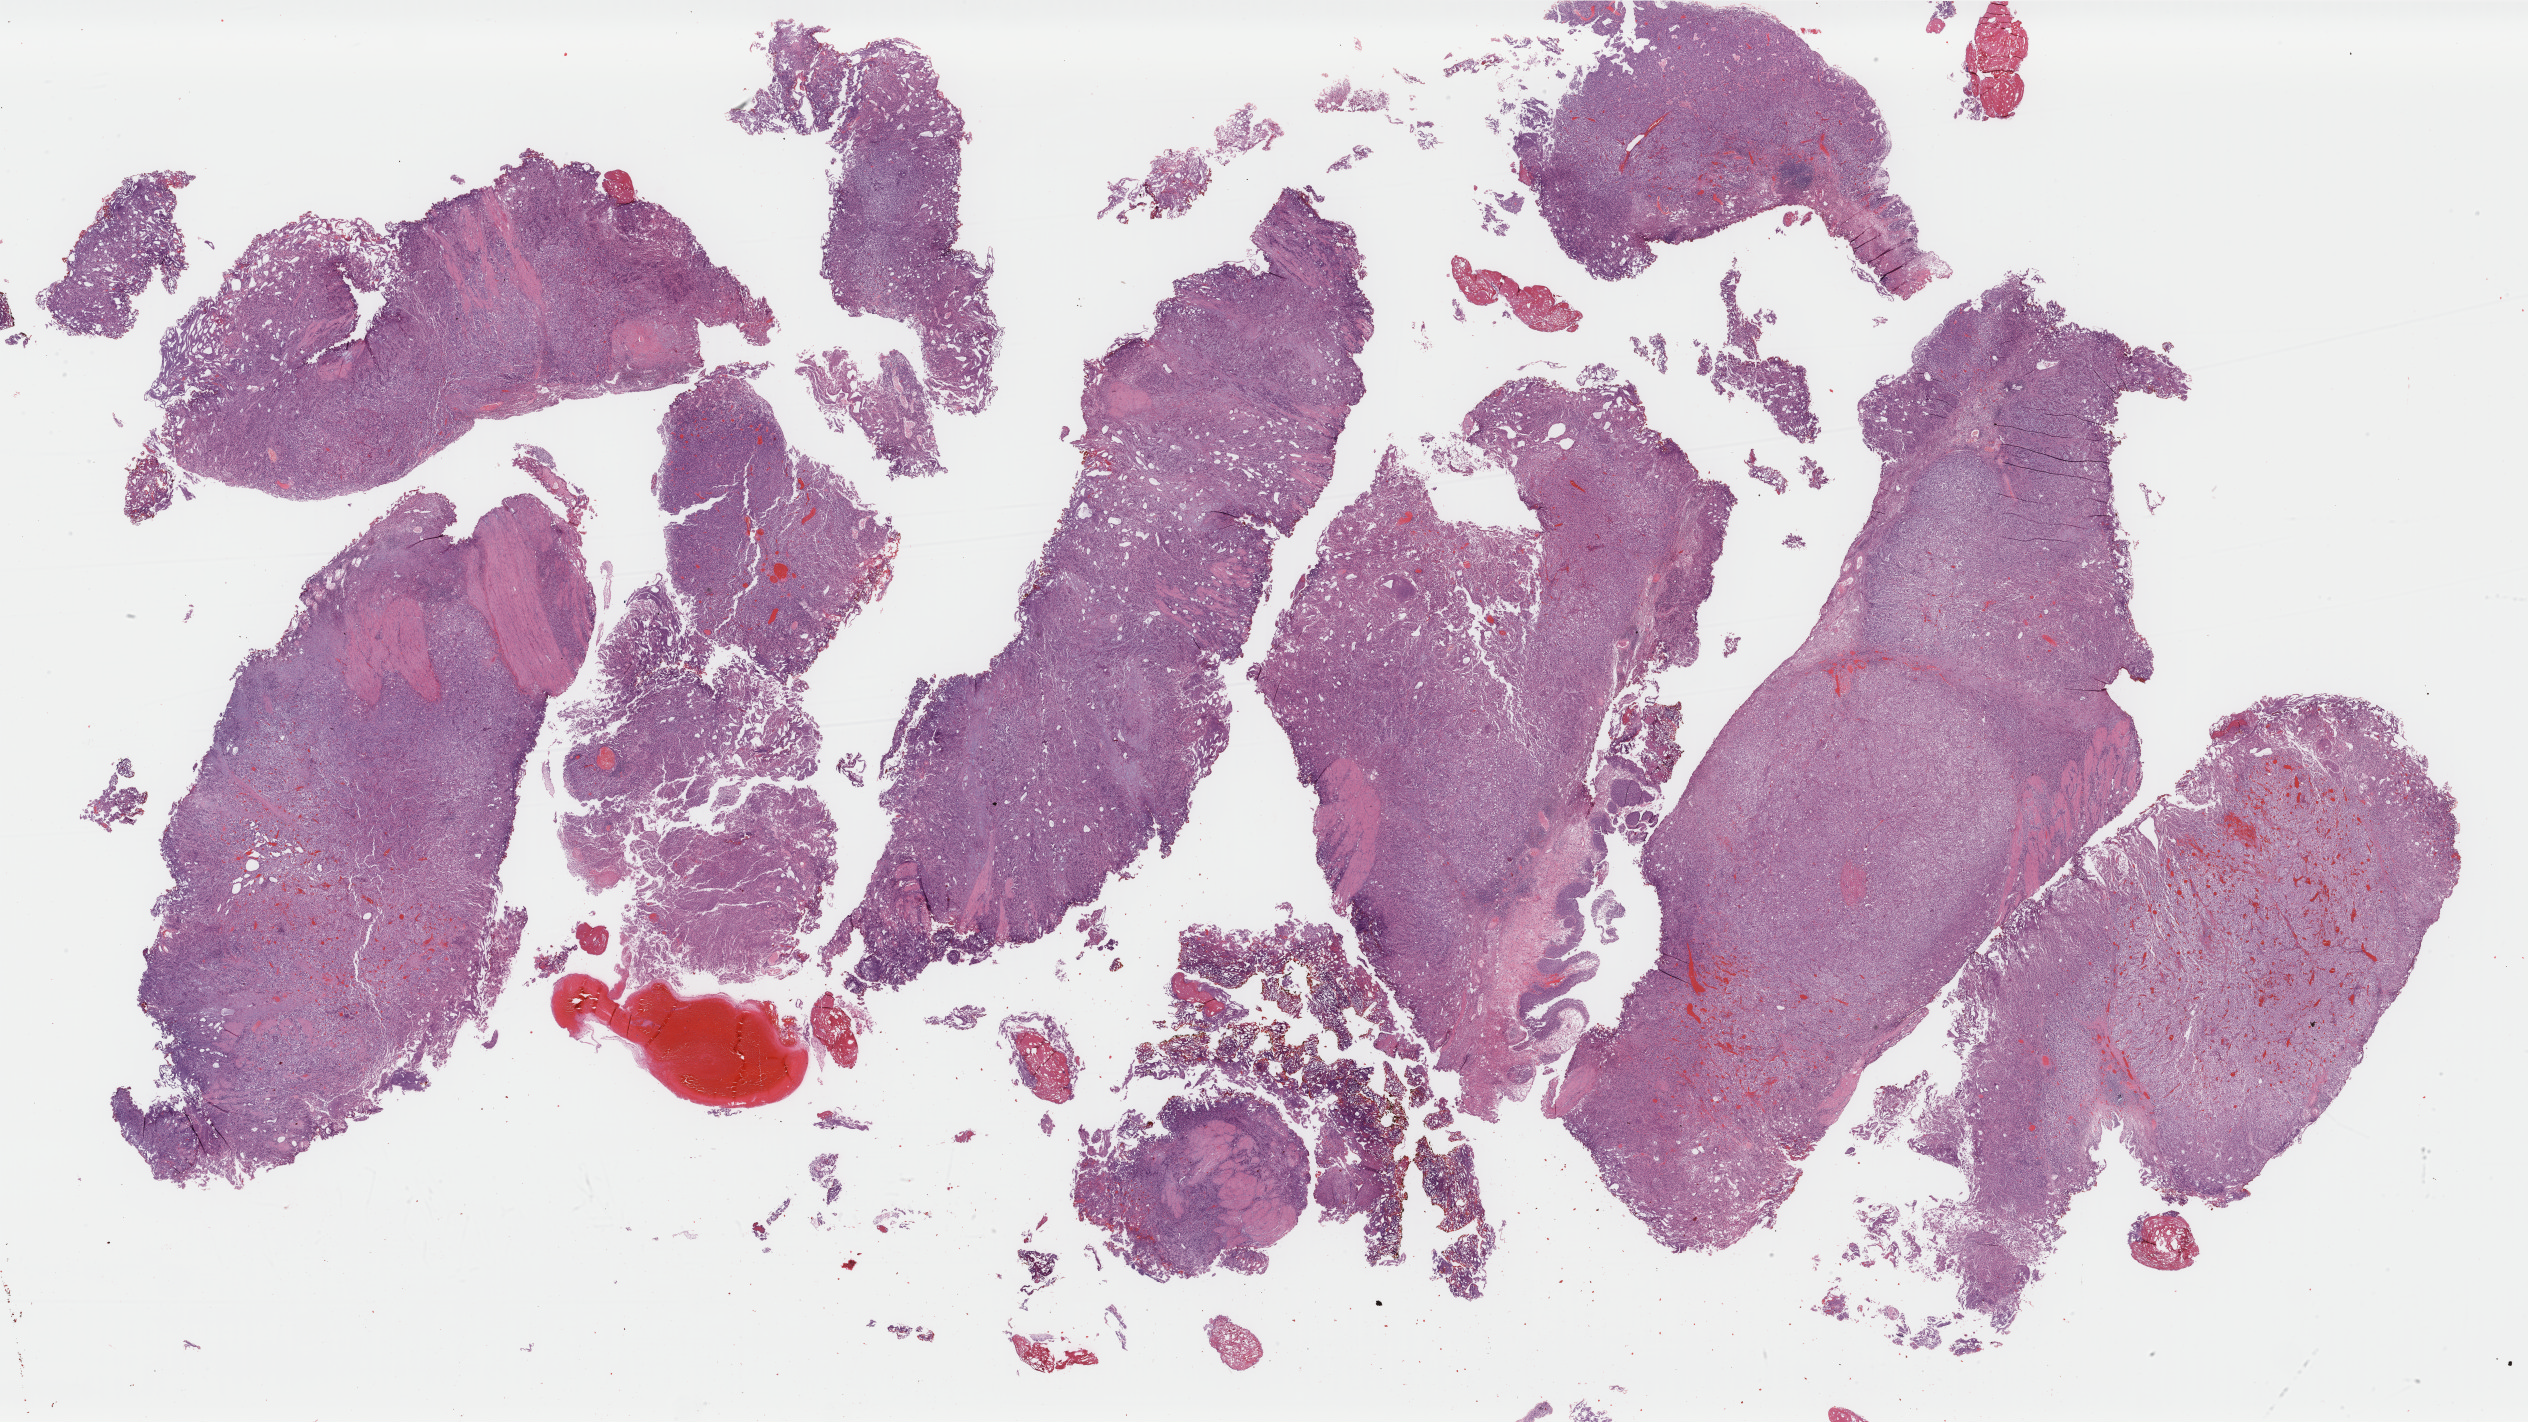
Digitized Hematoxylin and eosin (H&E) stained tissue section (whole slide), low-resolution overview of the scanned area, about 40.1 x 22.6 mm (acquisition: 40x scan). Formalin-fixed paraffin-embedded (FFPE) diagnostic section. Sample: primary tumour, bladder. Patient: male, age at initial diagnosis 51 years. Histologic grade: high grade.
Pathologic diagnosis: Transitional cell carcinoma. AJCC pathologic stage: II (6th edition). TNM: NX MX.